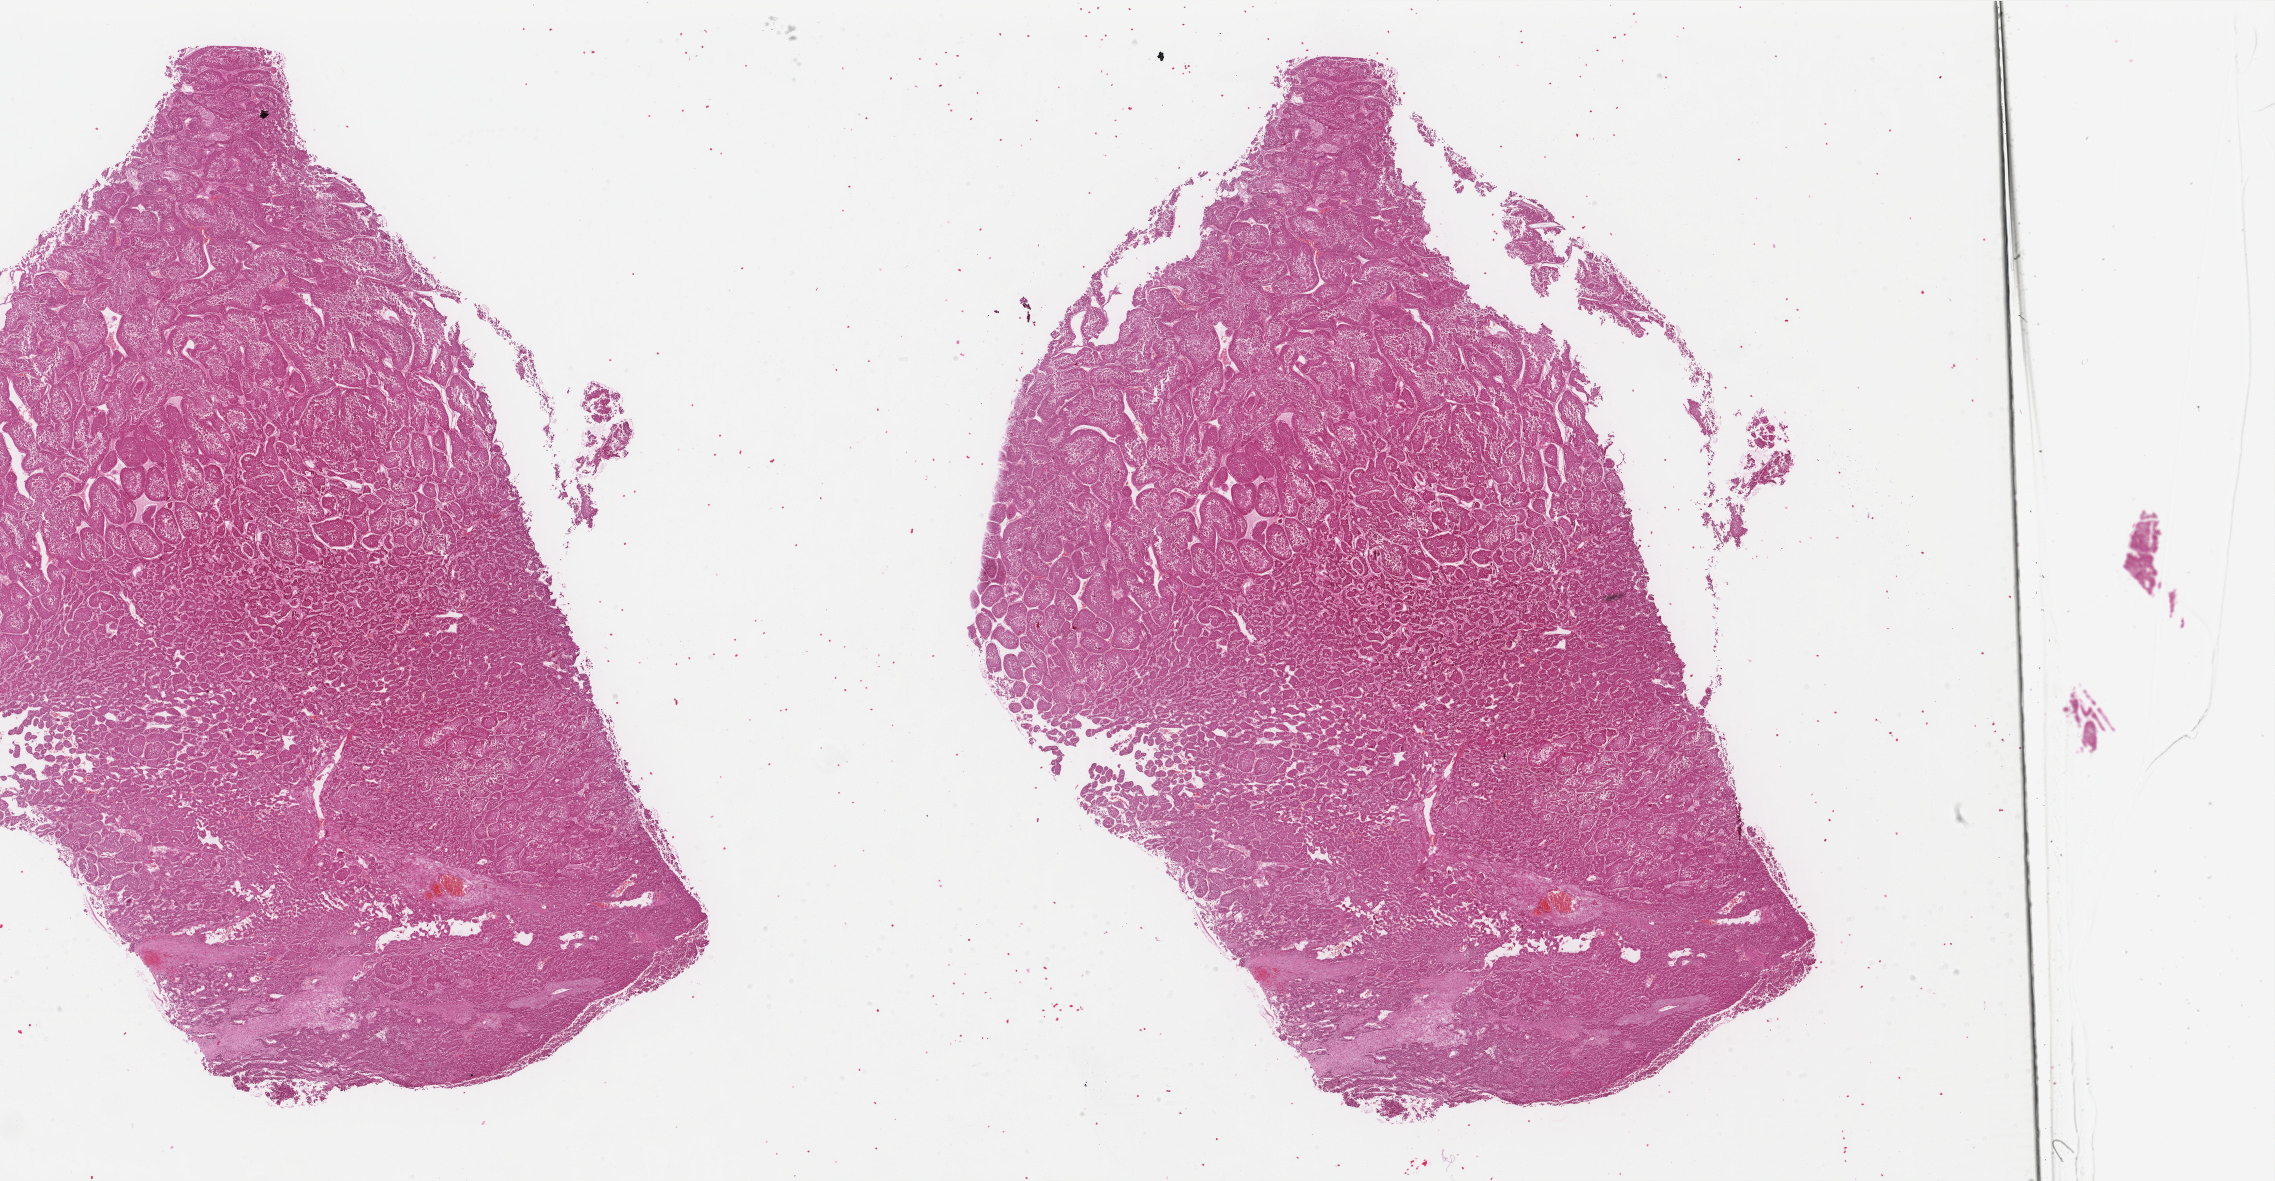
Digitized H&E tissue section (whole slide), whole scanned area (about 36.1 x 18.8 mm, slide scanned at 40x) shown as a low-resolution overview. Formalin-fixed paraffin-embedded (FFPE) diagnostic section. Primary tumour sample from the liver. Patient: male, age at initial diagnosis 69 years. Histologic grade: G2 (moderately differentiated).
Diagnosis: Hepatocellular carcinoma, NOS.